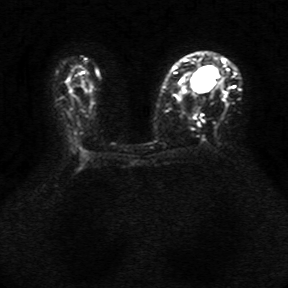
Breast MRI, one axial slice; slice 19 of 34 in the series (ordered by position); diffusion-weighted series; image 2 of 4 stored at this slice position (different b-values; order by instance number); 1.5 T; 5 mm slice thickness; 288 × 288 image matrix, field of view 340 × 340 mm. Female patient.
Structures marked on this image (outlined manually by an expert reader):
- tumour on diffusion-weighted imaging: bounding box [x1, y1, x2, y2] px = [193, 71, 214, 91]